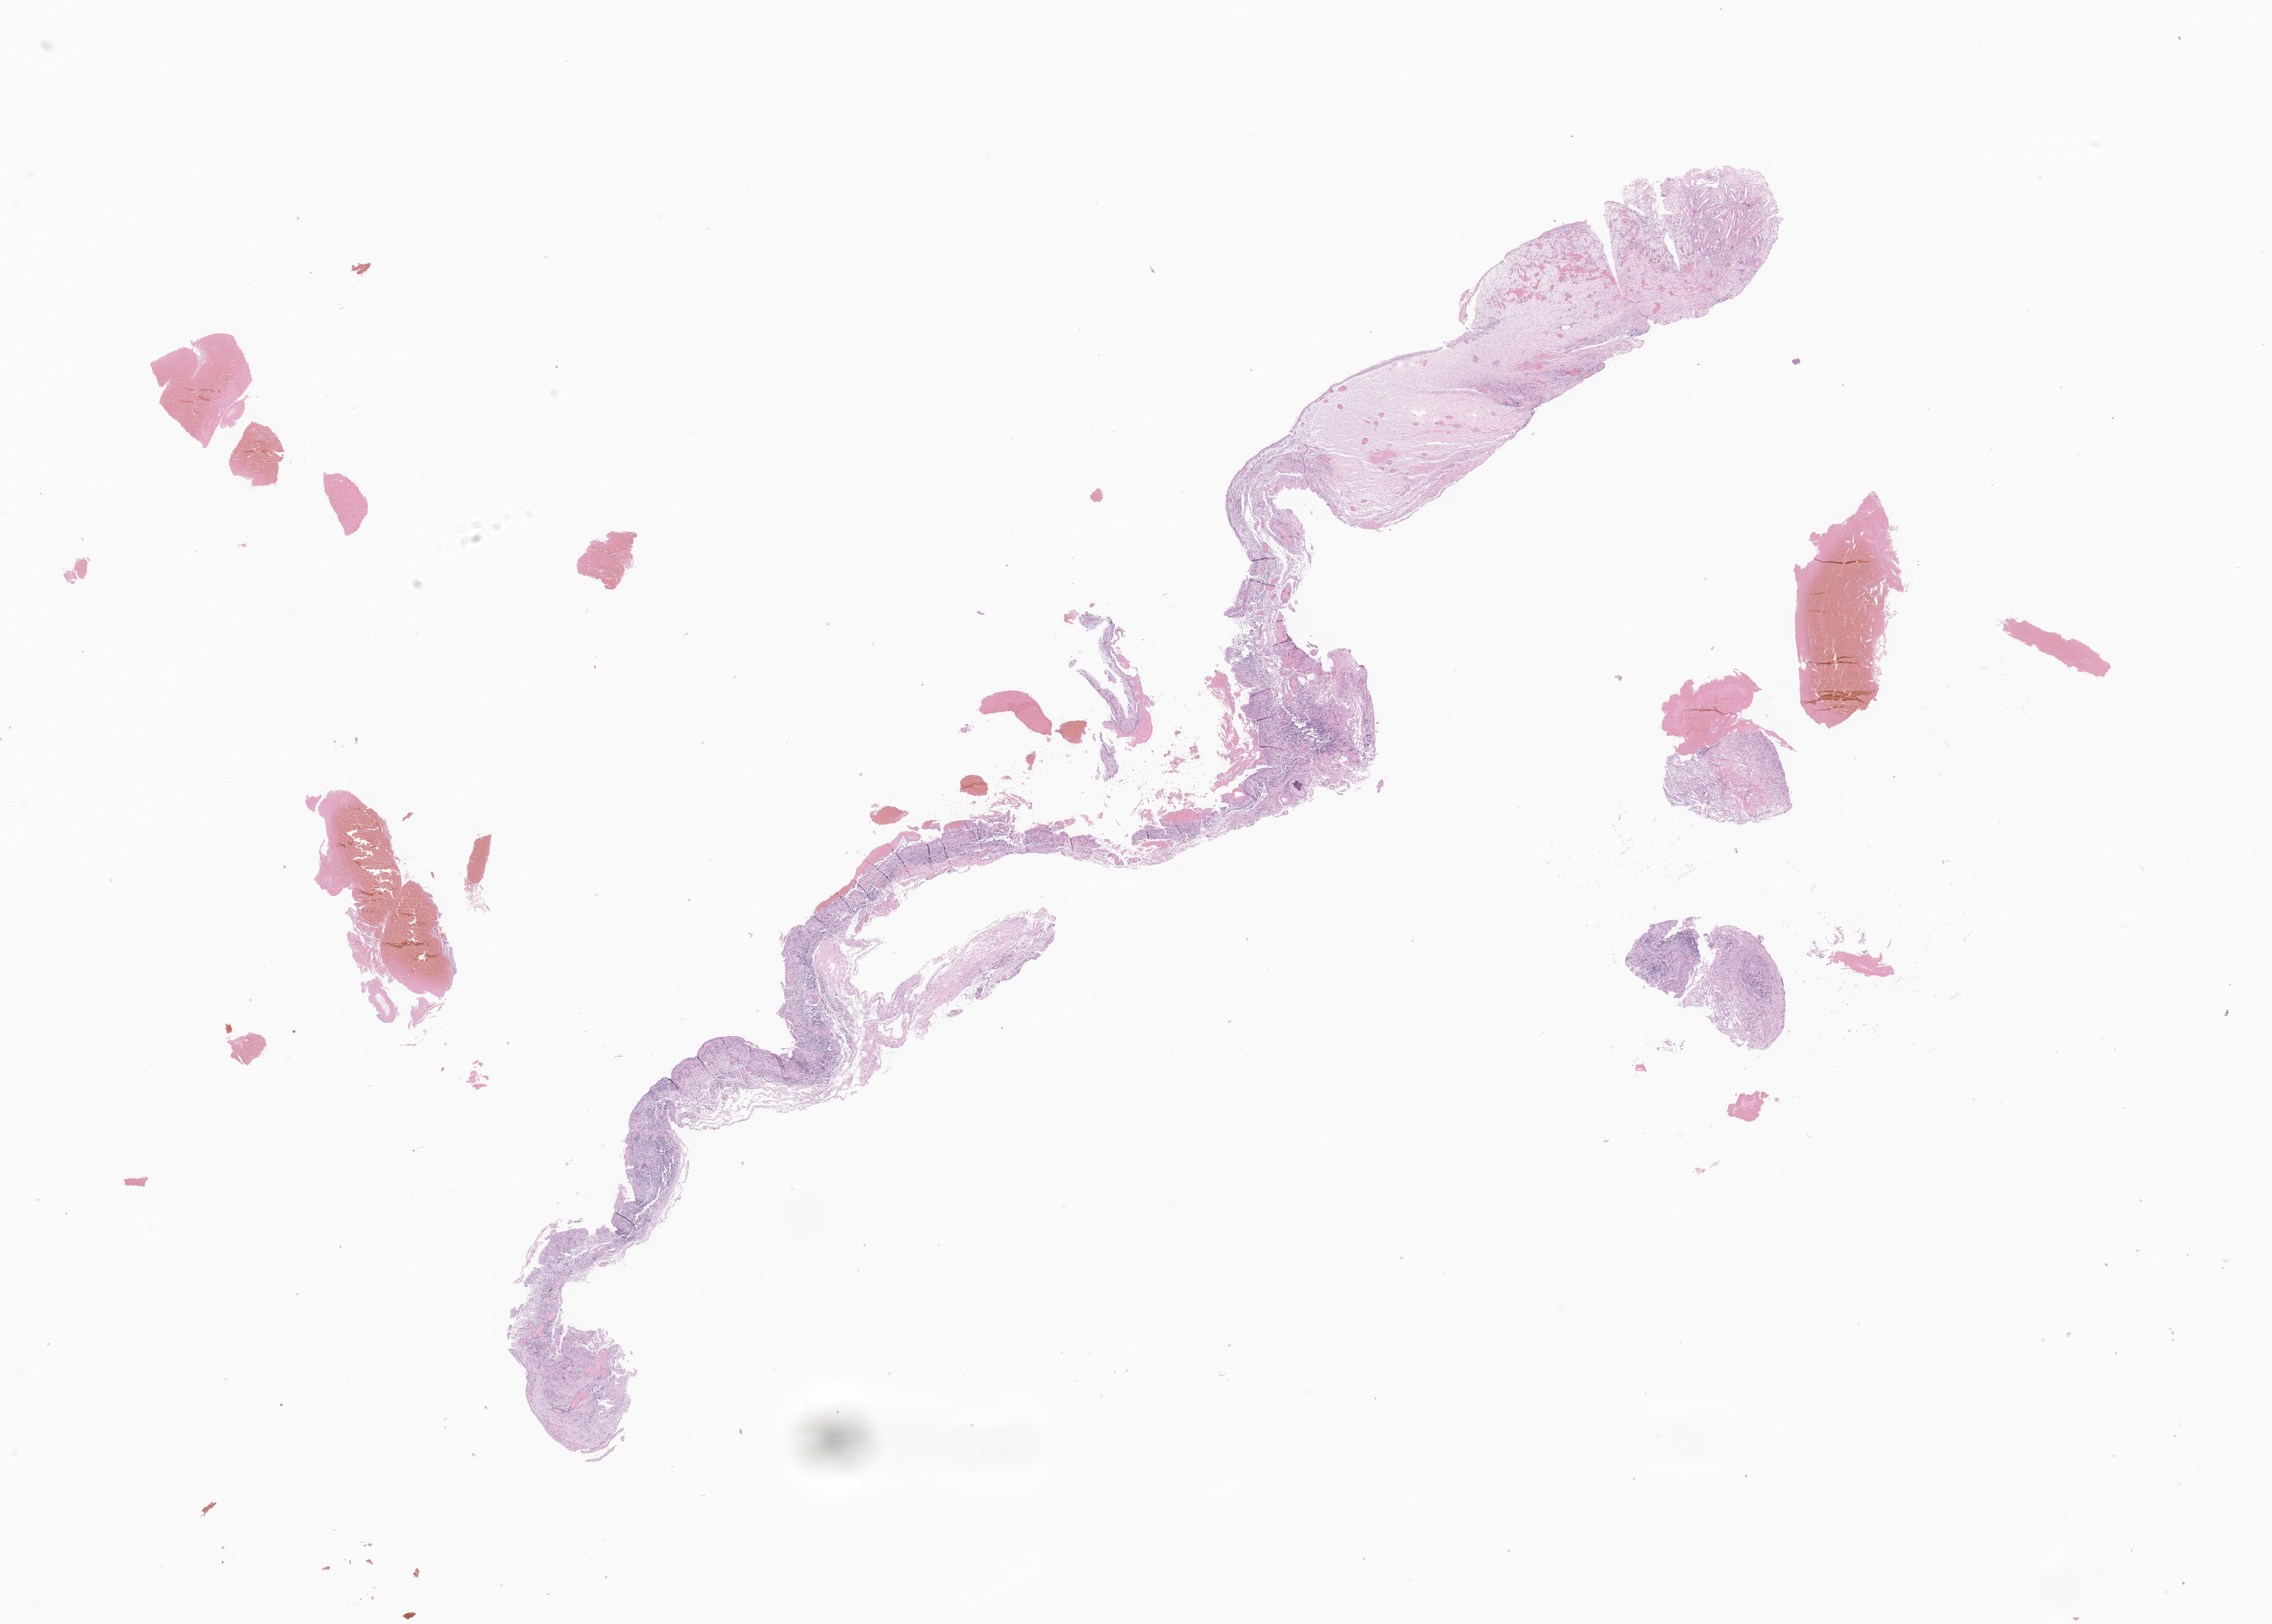
Digitized haematoxylin and eosin-stained section of tumor tissue from the brain, shown as a low-resolution overview of the whole scanned area (about 26.0 x 18.6 mm); formalin-fixed paraffin-embedded section. Patient: male, age 131 months (10 years 11 months).
Diagnosis: Craniopharyngioma, adamantinomatous.